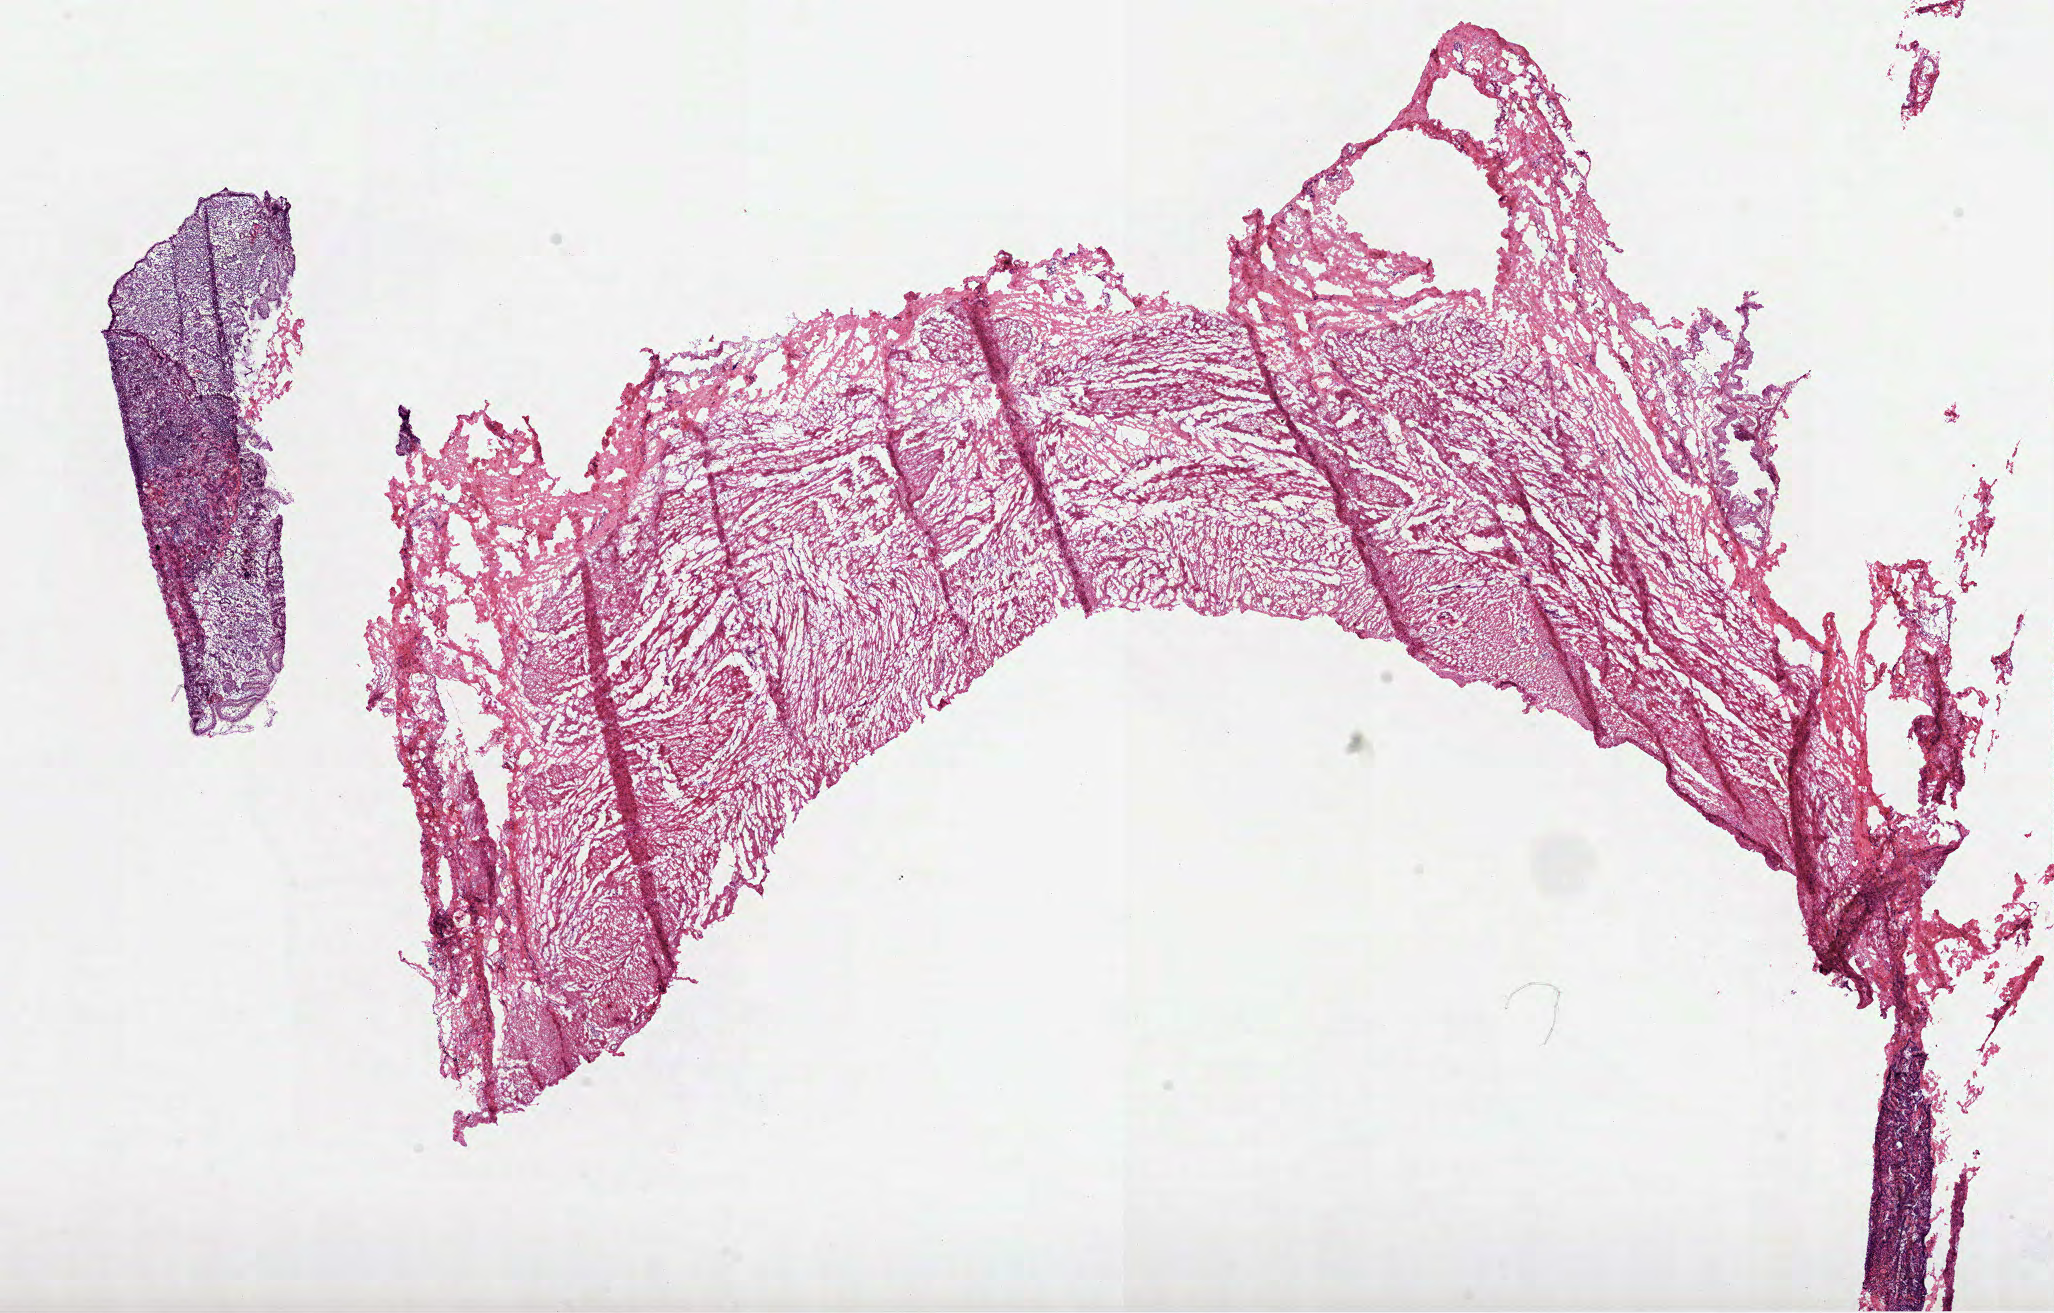
Digitized Hematoxylin and eosin (H&E) stained tissue section (whole slide) — a low-resolution overview of the entire scanned area, about 16.6 x 10.6 mm (slide scanned at 40x), frozen section from the top of the tissue portion, sample: solid tissue normal (non-tumour tissue), stomach. Male, age 58 years at initial diagnosis.
* this section: solid tissue normal (non-tumour) sample from the same patient
* patient diagnosis: Adenocarcinoma, NOS (cardia, NOS)